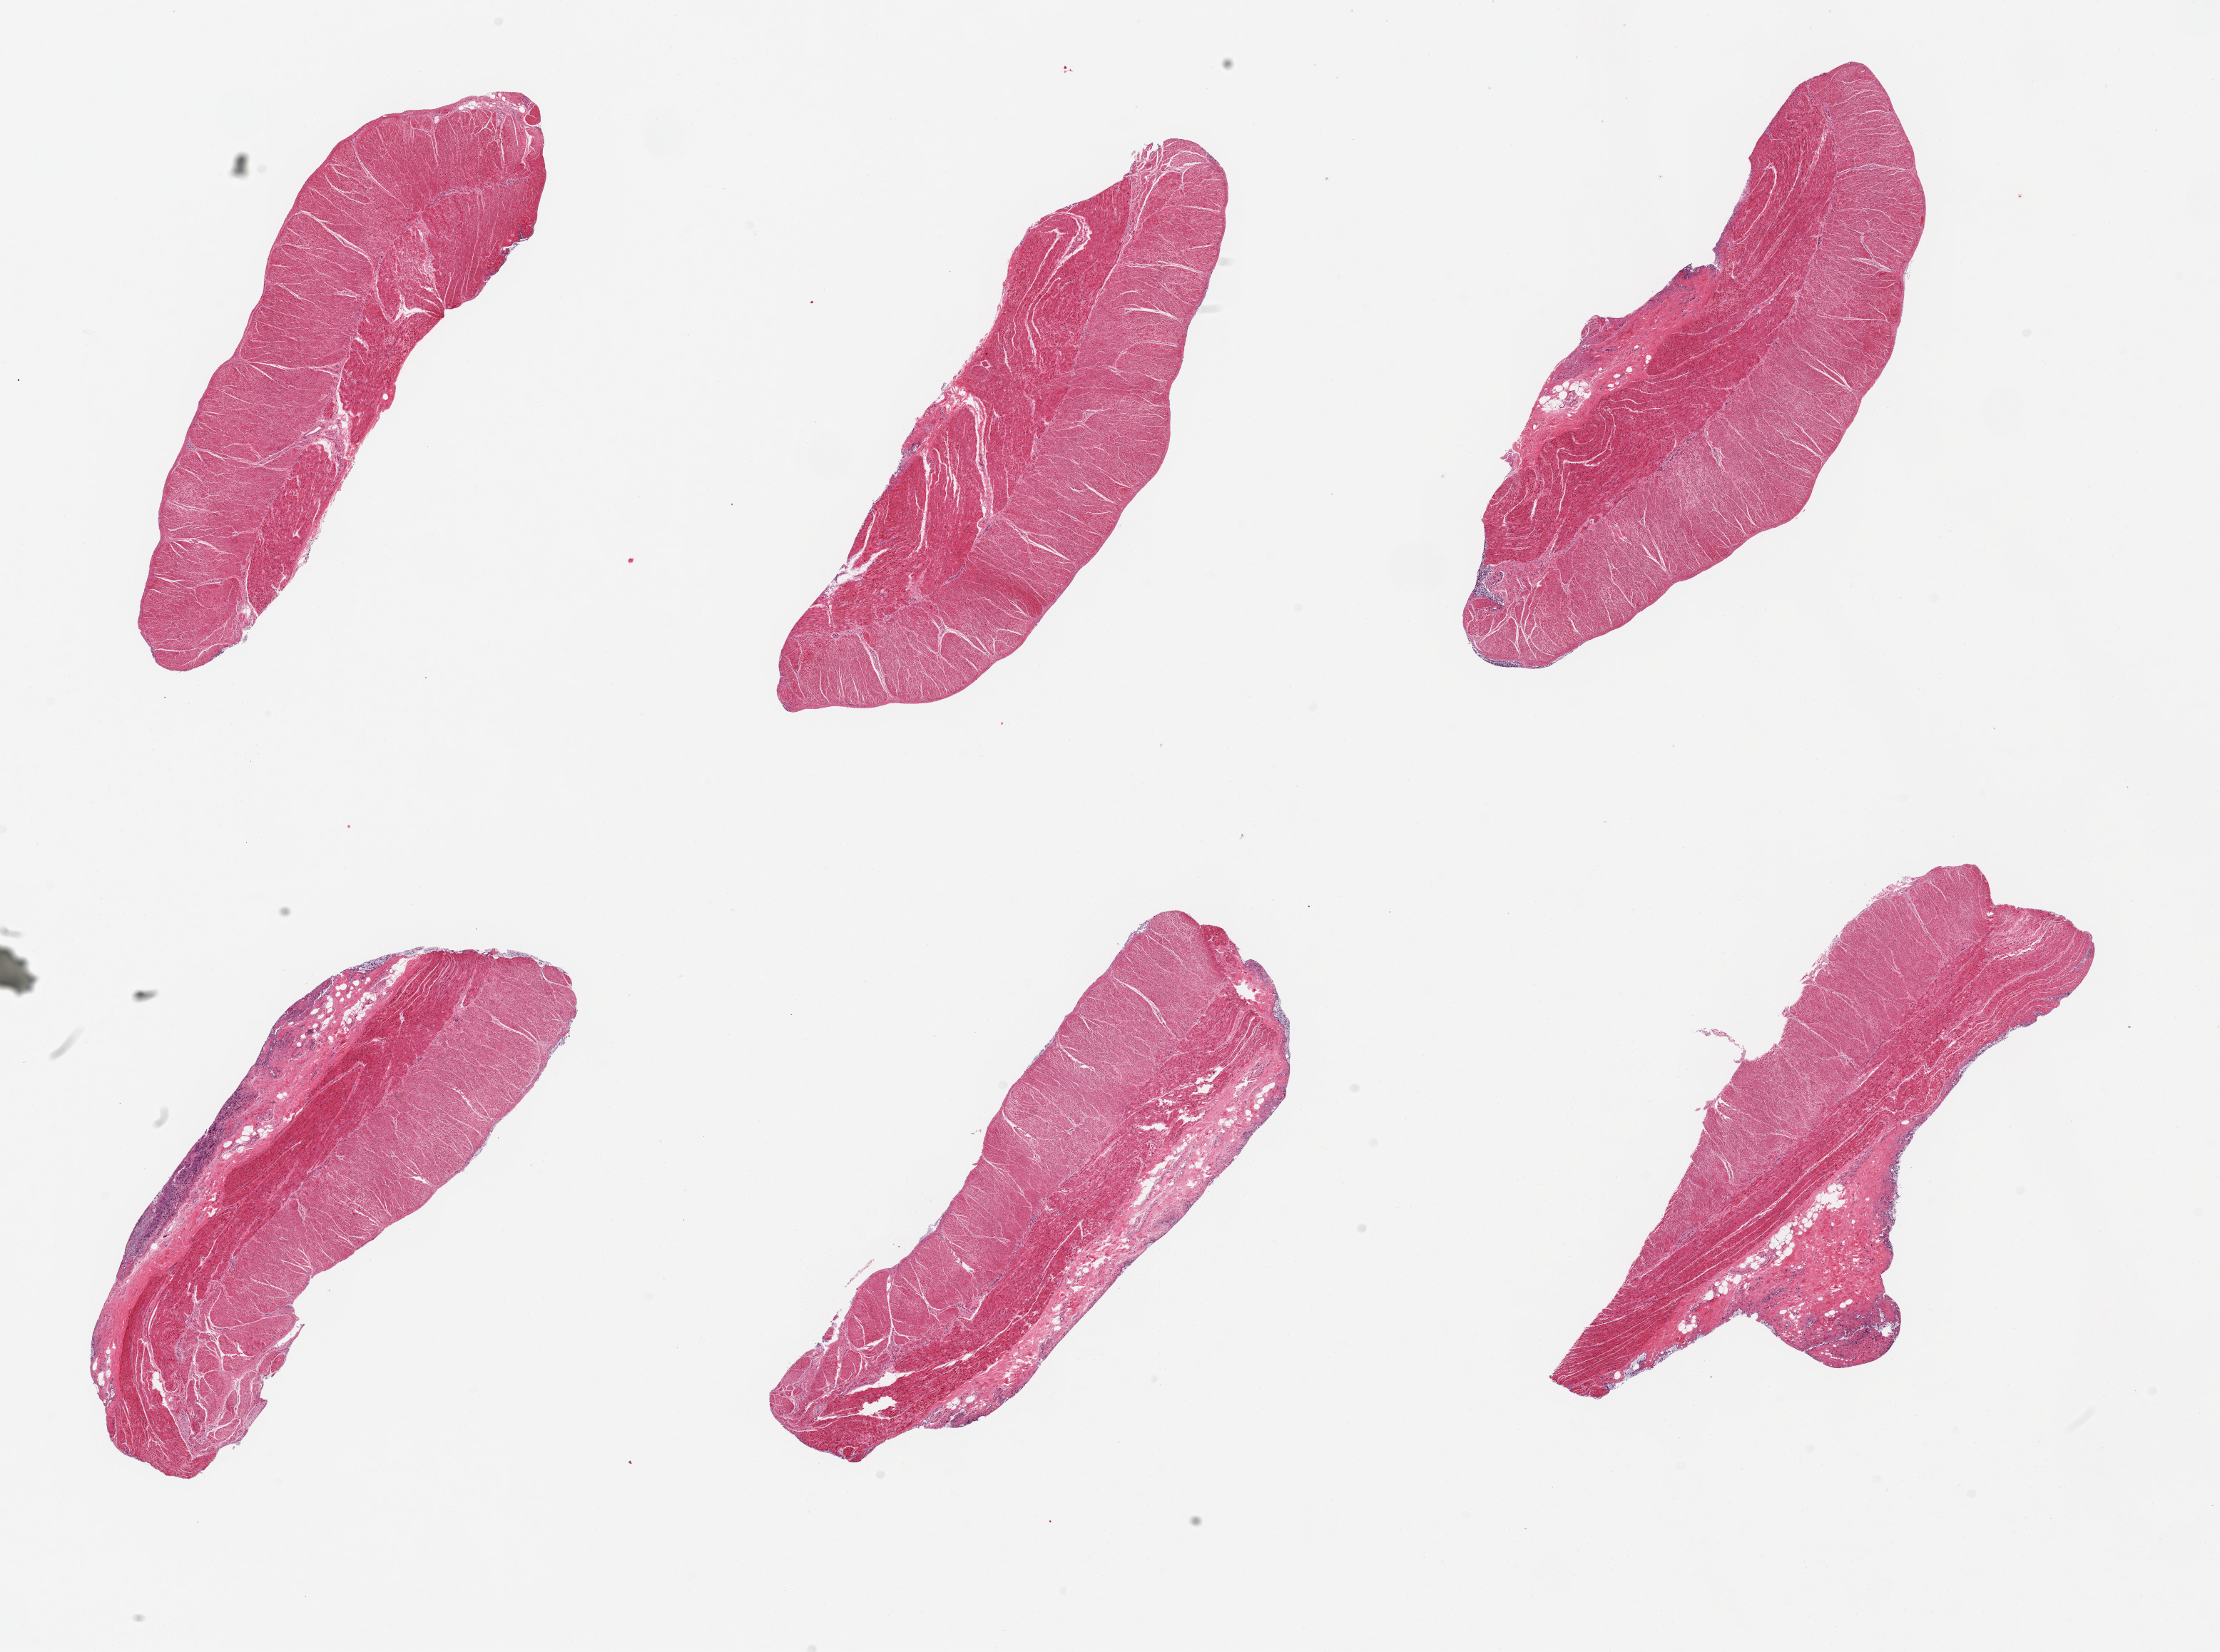
Digitized hematoxylin and eosin (H&E)-stained section, shown as a low-resolution overview of the whole scanned area (about 24.6 x 18.3 mm); PAXgene-fixed, paraffin-embedded tissue; target tissue: sigmoid colon; donor tissue sample. Male donor.
Reviewer comment on this tissue sample: 6 pieces; muscularis with up to 20% submucosal stroma.